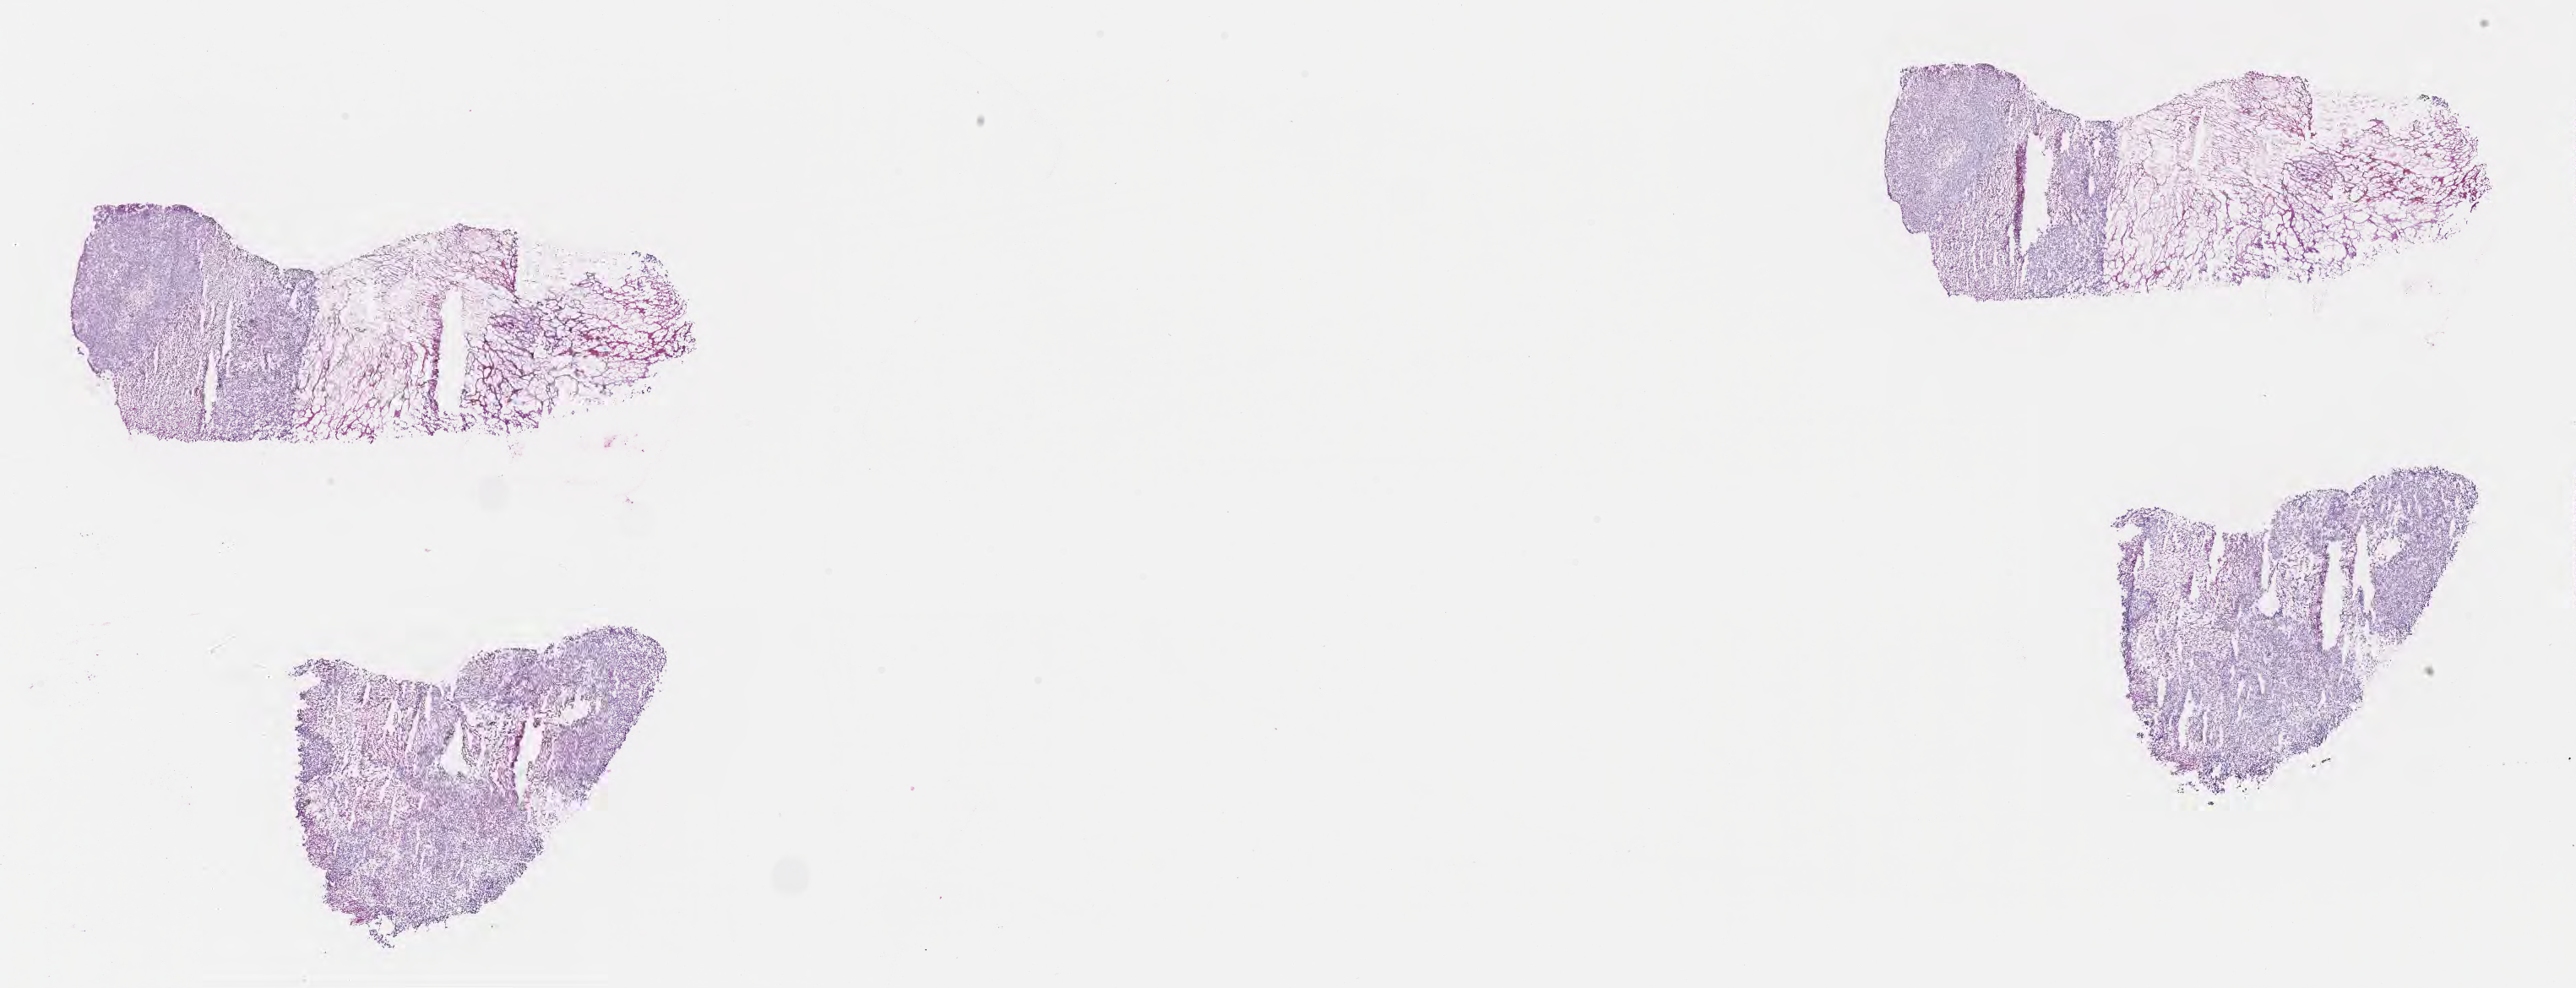
Whole-slide image, hematoxylin and eosin (H&E) stain — whole scanned area (about 24.7 x 9.5 mm) shown as a low-resolution overview; cryosection; metastatic tumor tissue, resected from brain. Male, age 9 years at initial diagnosis. Slide review estimates, as recorded: tumor cells 60%, tumor nuclei 70%, stromal cells 30%, necrosis 10%, normal cells 0%. Inflammatory infiltration, as recorded: lymphocyte infiltration 0%, monocyte infiltration 0%, neutrophil infiltration 0%.
Patient diagnosis (primary): Undifferentiated sarcoma. Section: bottom of the tissue portion.